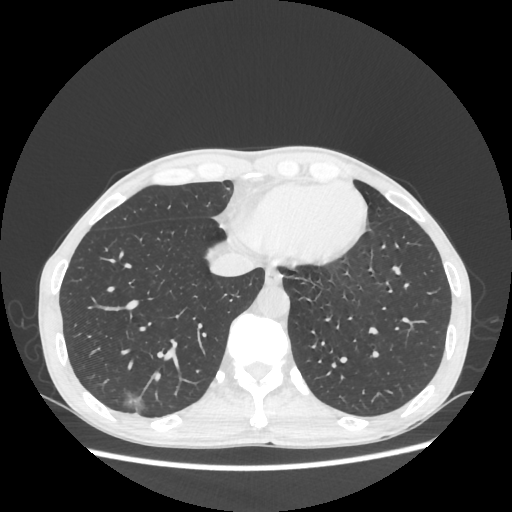
Chest CT, one axial slice; position 74 of 270 along the scan axis; lung window (W 1500 / L -600 HU); 512 × 512 image matrix. Patient: male, 60 years. From the clinical record (not read from this slice): clinical TNM (as recorded): T1c N0 M0; histopathological grade: G2.
Annotated regions visible in this slice (rectangle marked by the reading radiologist):
- lung tumour (recorded histology: adenocarcinoma): box from (x=111, y=380) to (x=156, y=418) px